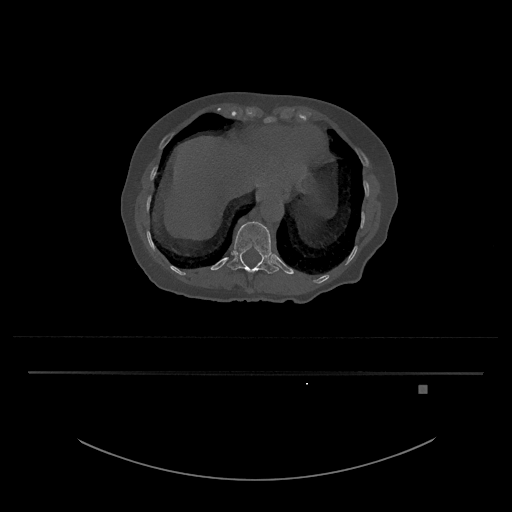
CT including the spine, one axial slice; position 618 of 797 along the scan axis; reconstruction kernel Br40s/3; 120 kVp; bone window (W 1800 / L 400 HU); 512 × 512 image matrix, field of view 500 × 500 mm. Patient: female, 57 years. From the clinical record (not read from this slice): primary cancer: cervical.
Structures marked on this image (semi-automatically segmented with operator editing):
- T12 vertebra: bounding box (x1, y1, x2, y2) in pixels: (227, 221, 279, 274)